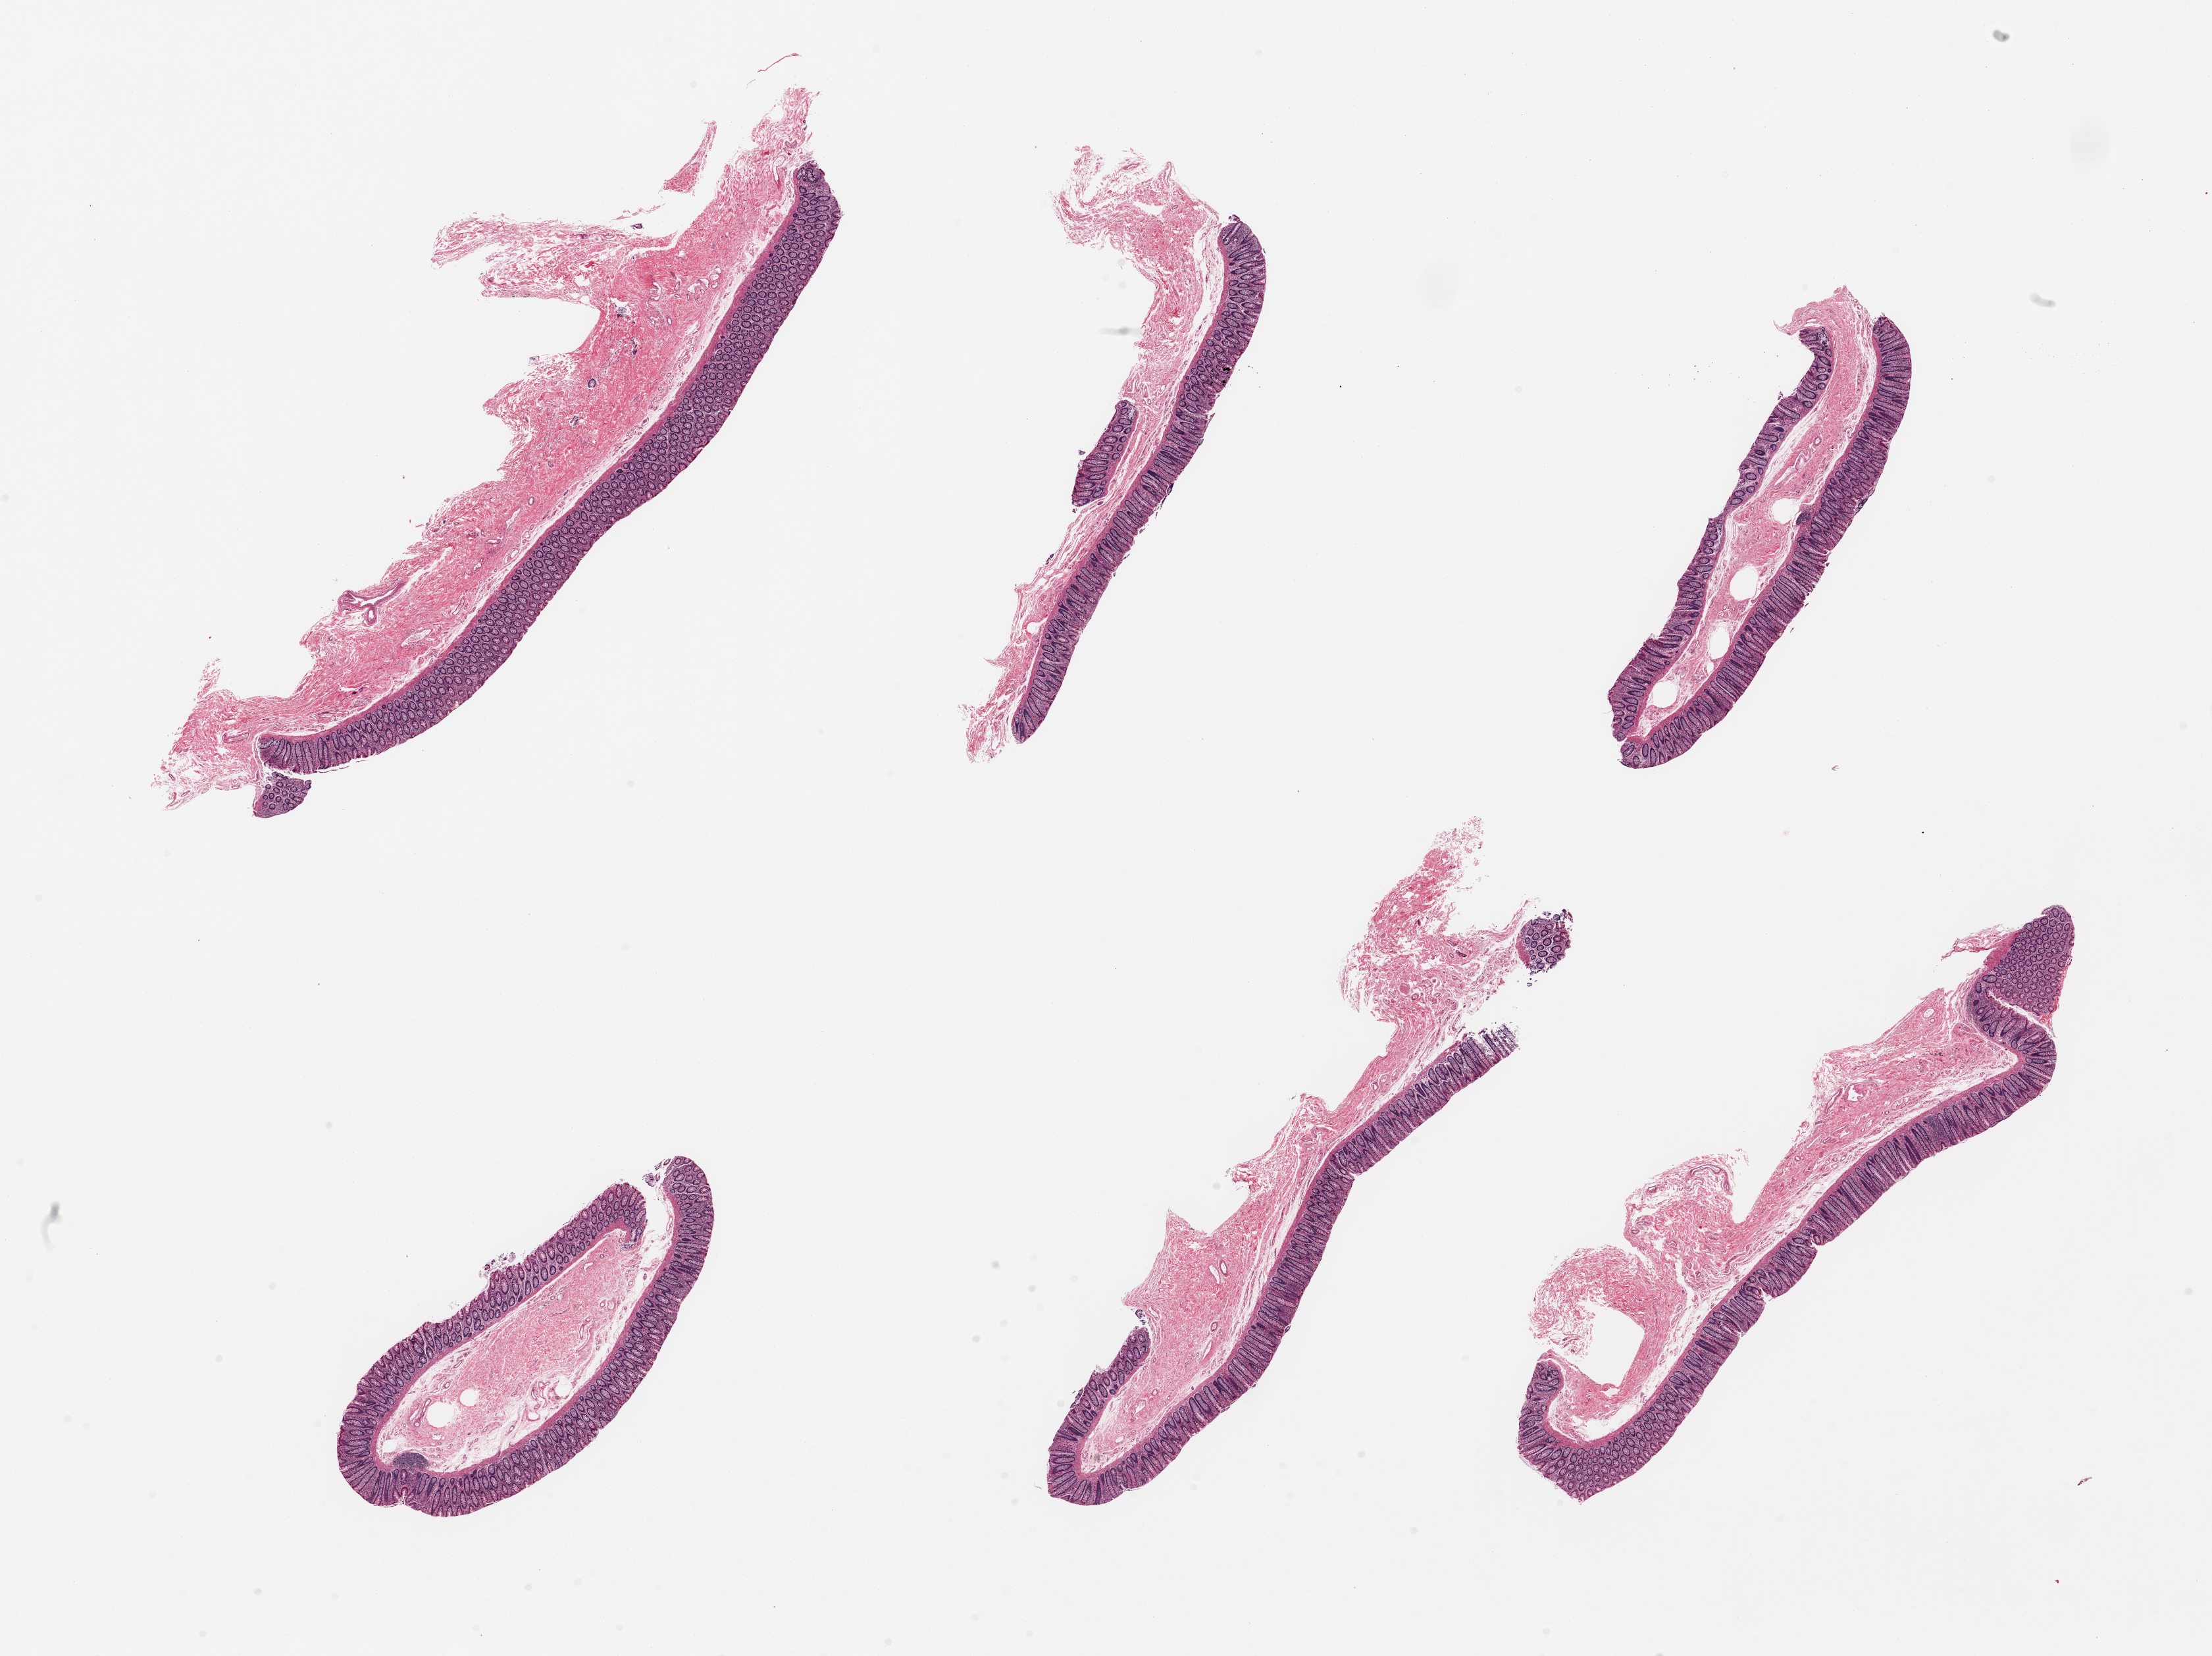
Digitized H&E-stained section — a low-resolution overview of the entire scanned area, about 26.6 x 19.9 mm (acquisition: 20x scan); PAXgene-fixed paraffin-embedded (PFPE) section; sampled site (target tissue): transverse colon; tissue donor sample. Male donor.
• pathologist's review note for this sample: 6 pieces; essentially well preserved mucosa